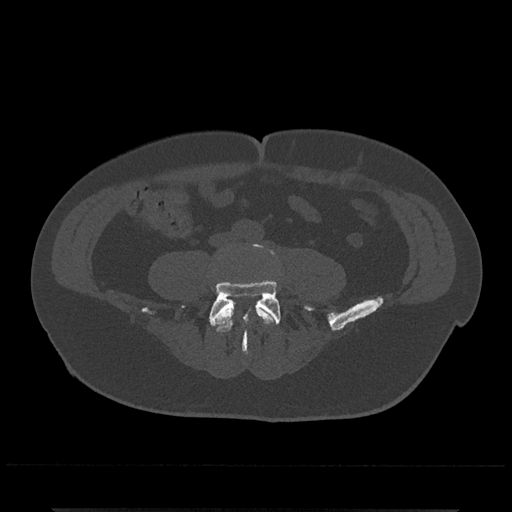
CT including the spine, one axial slice; position 111 of 797 along the scan axis; 120 kVp; bone window (W 1800 / L 400 HU); 512 × 512 image matrix, field of view 393 × 393 mm. Male patient, age 67 years. Case-level facts recorded for this patient, not image findings: primary cancer: prostate.
Structures marked on this image (semi-automatically segmented with operator editing):
- L4 vertebra: bounding box [x1, y1, x2, y2] px = [212, 301, 278, 332]
- L5 vertebra: [209, 243, 313, 352]